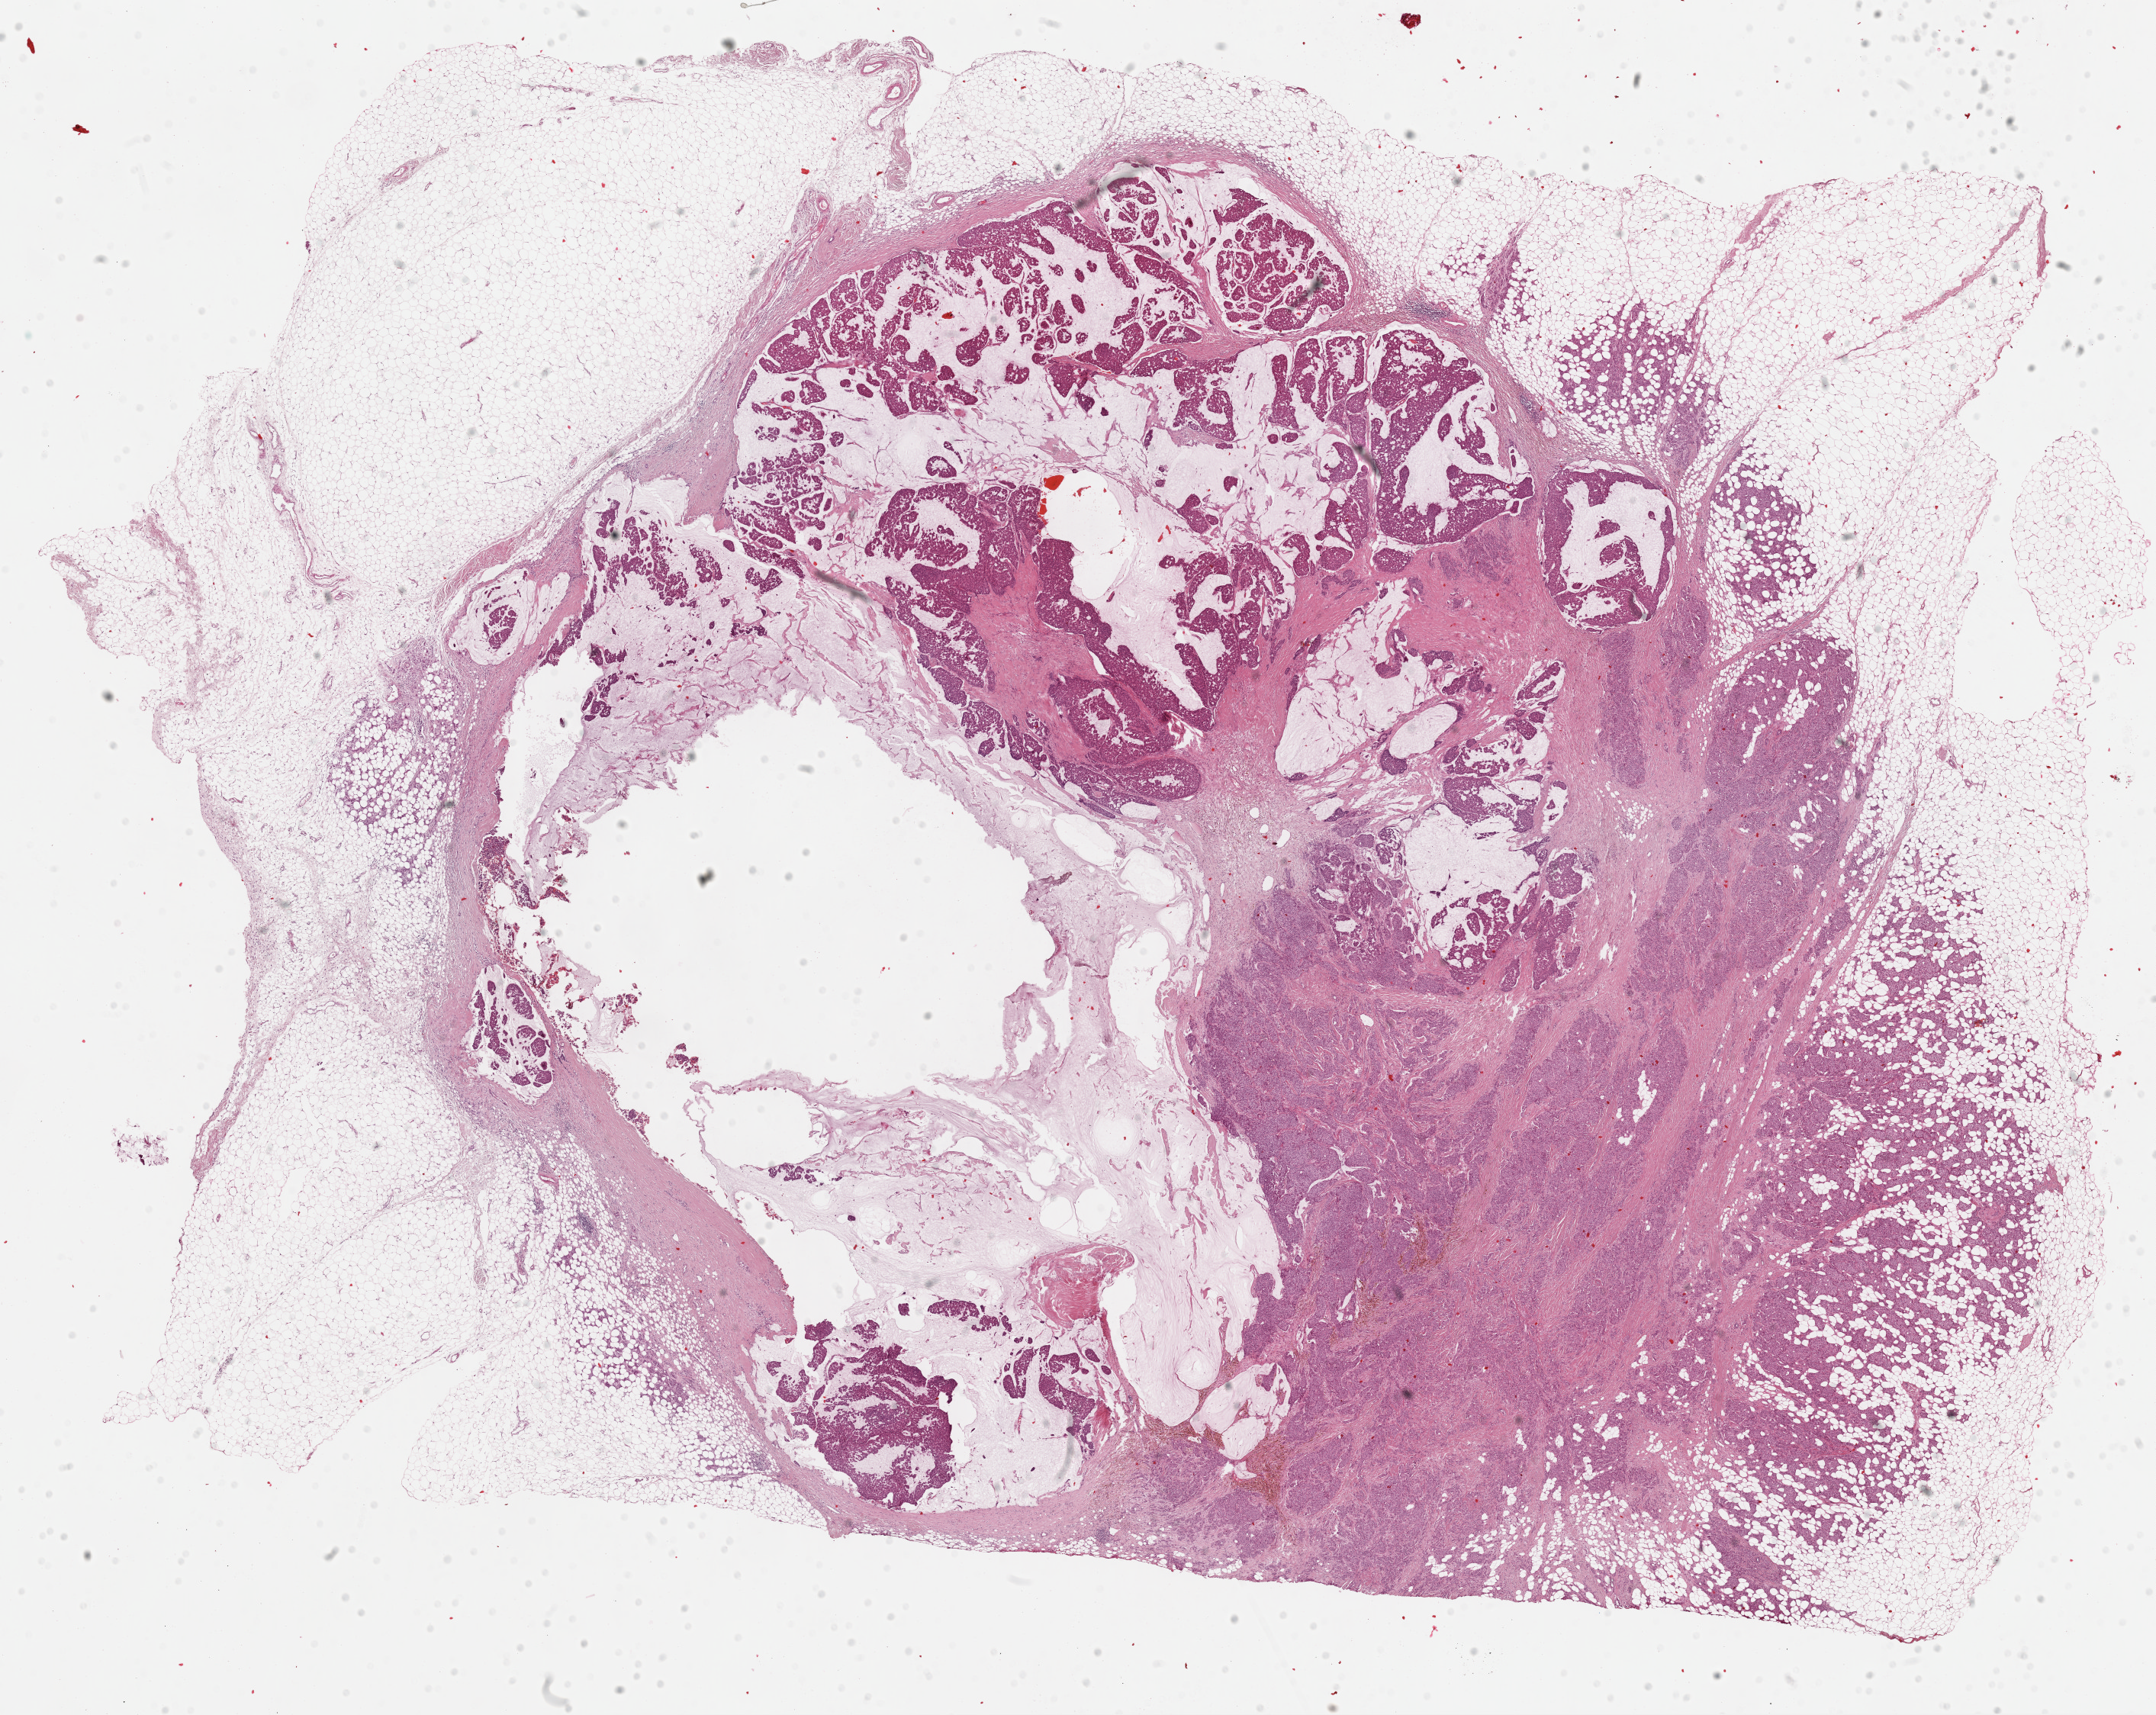
H&E whole-slide image, a low-resolution overview of the entire scanned area, about 22.3 x 17.8 mm (from a 40x scan); formalin-fixed paraffin-embedded (FFPE) diagnostic section; primary tumour sample from the breast. Female, age 84 years at initial diagnosis.
- AJCC pathologic stage: IIA (7th edition)
- lymph nodes positive (case pathology): 0 of 1 examined
- diagnosis: Mucinous adenocarcinoma